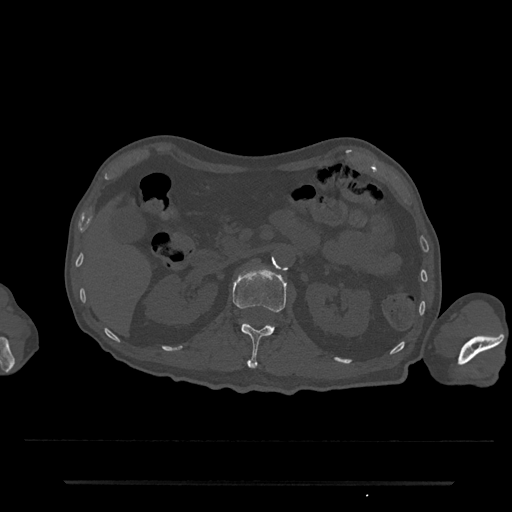
CT including the spine, one axial slice. Slice 118 of 797 in the series (ordered by position). Reconstruction kernel Br40s/3. Bone window (W 1800 / L 400 HU). 0.5 mm slice thickness. 512 × 512 image matrix, field of view 427 × 427 mm. Patient: male, 74 years. Case-level facts recorded for this patient, not image findings: primary cancer: prostate.
Annotated regions visible in this slice (semi-automatically segmented with operator editing):
- L1 vertebra: bounding box <233,267,287,369> (left, top, right, bottom; pixels)